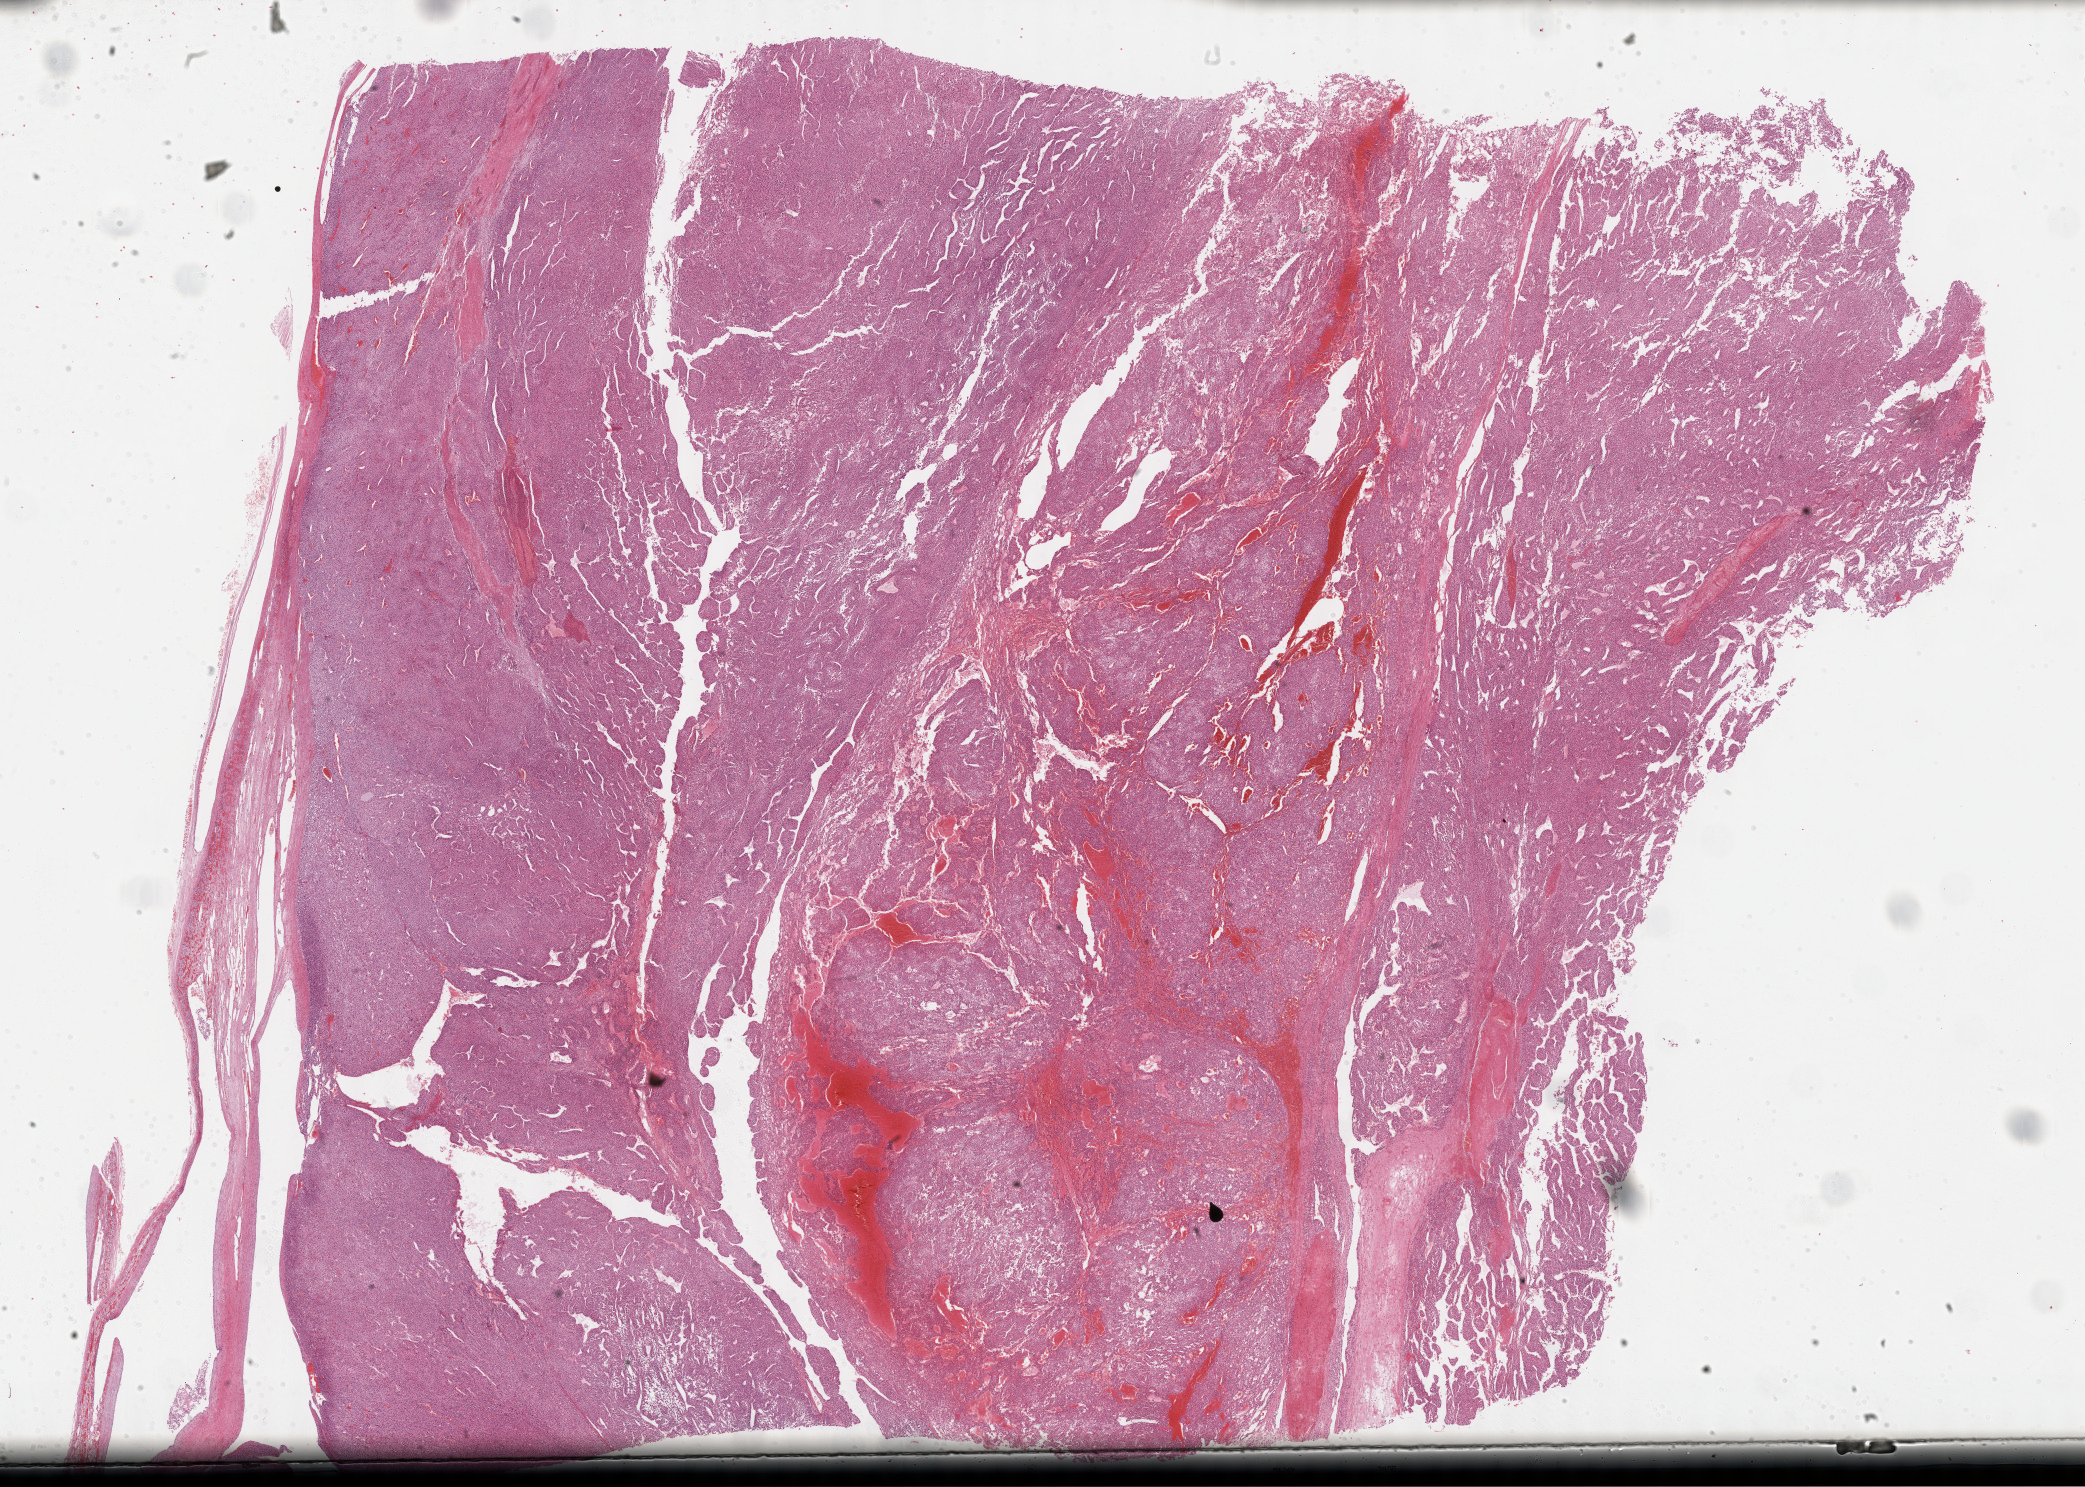
Whole-slide histology image, H&E-stained, low-resolution overview of the scanned area, about 33.7 x 24.1 mm (from a 40x scan); formalin-fixed paraffin-embedded (FFPE) diagnostic section; adrenal cortex, primary tumour sample. Male patient; age at initial diagnosis 37 years.
Histologic diagnosis: Adrenal cortical carcinoma (cortex of adrenal gland).